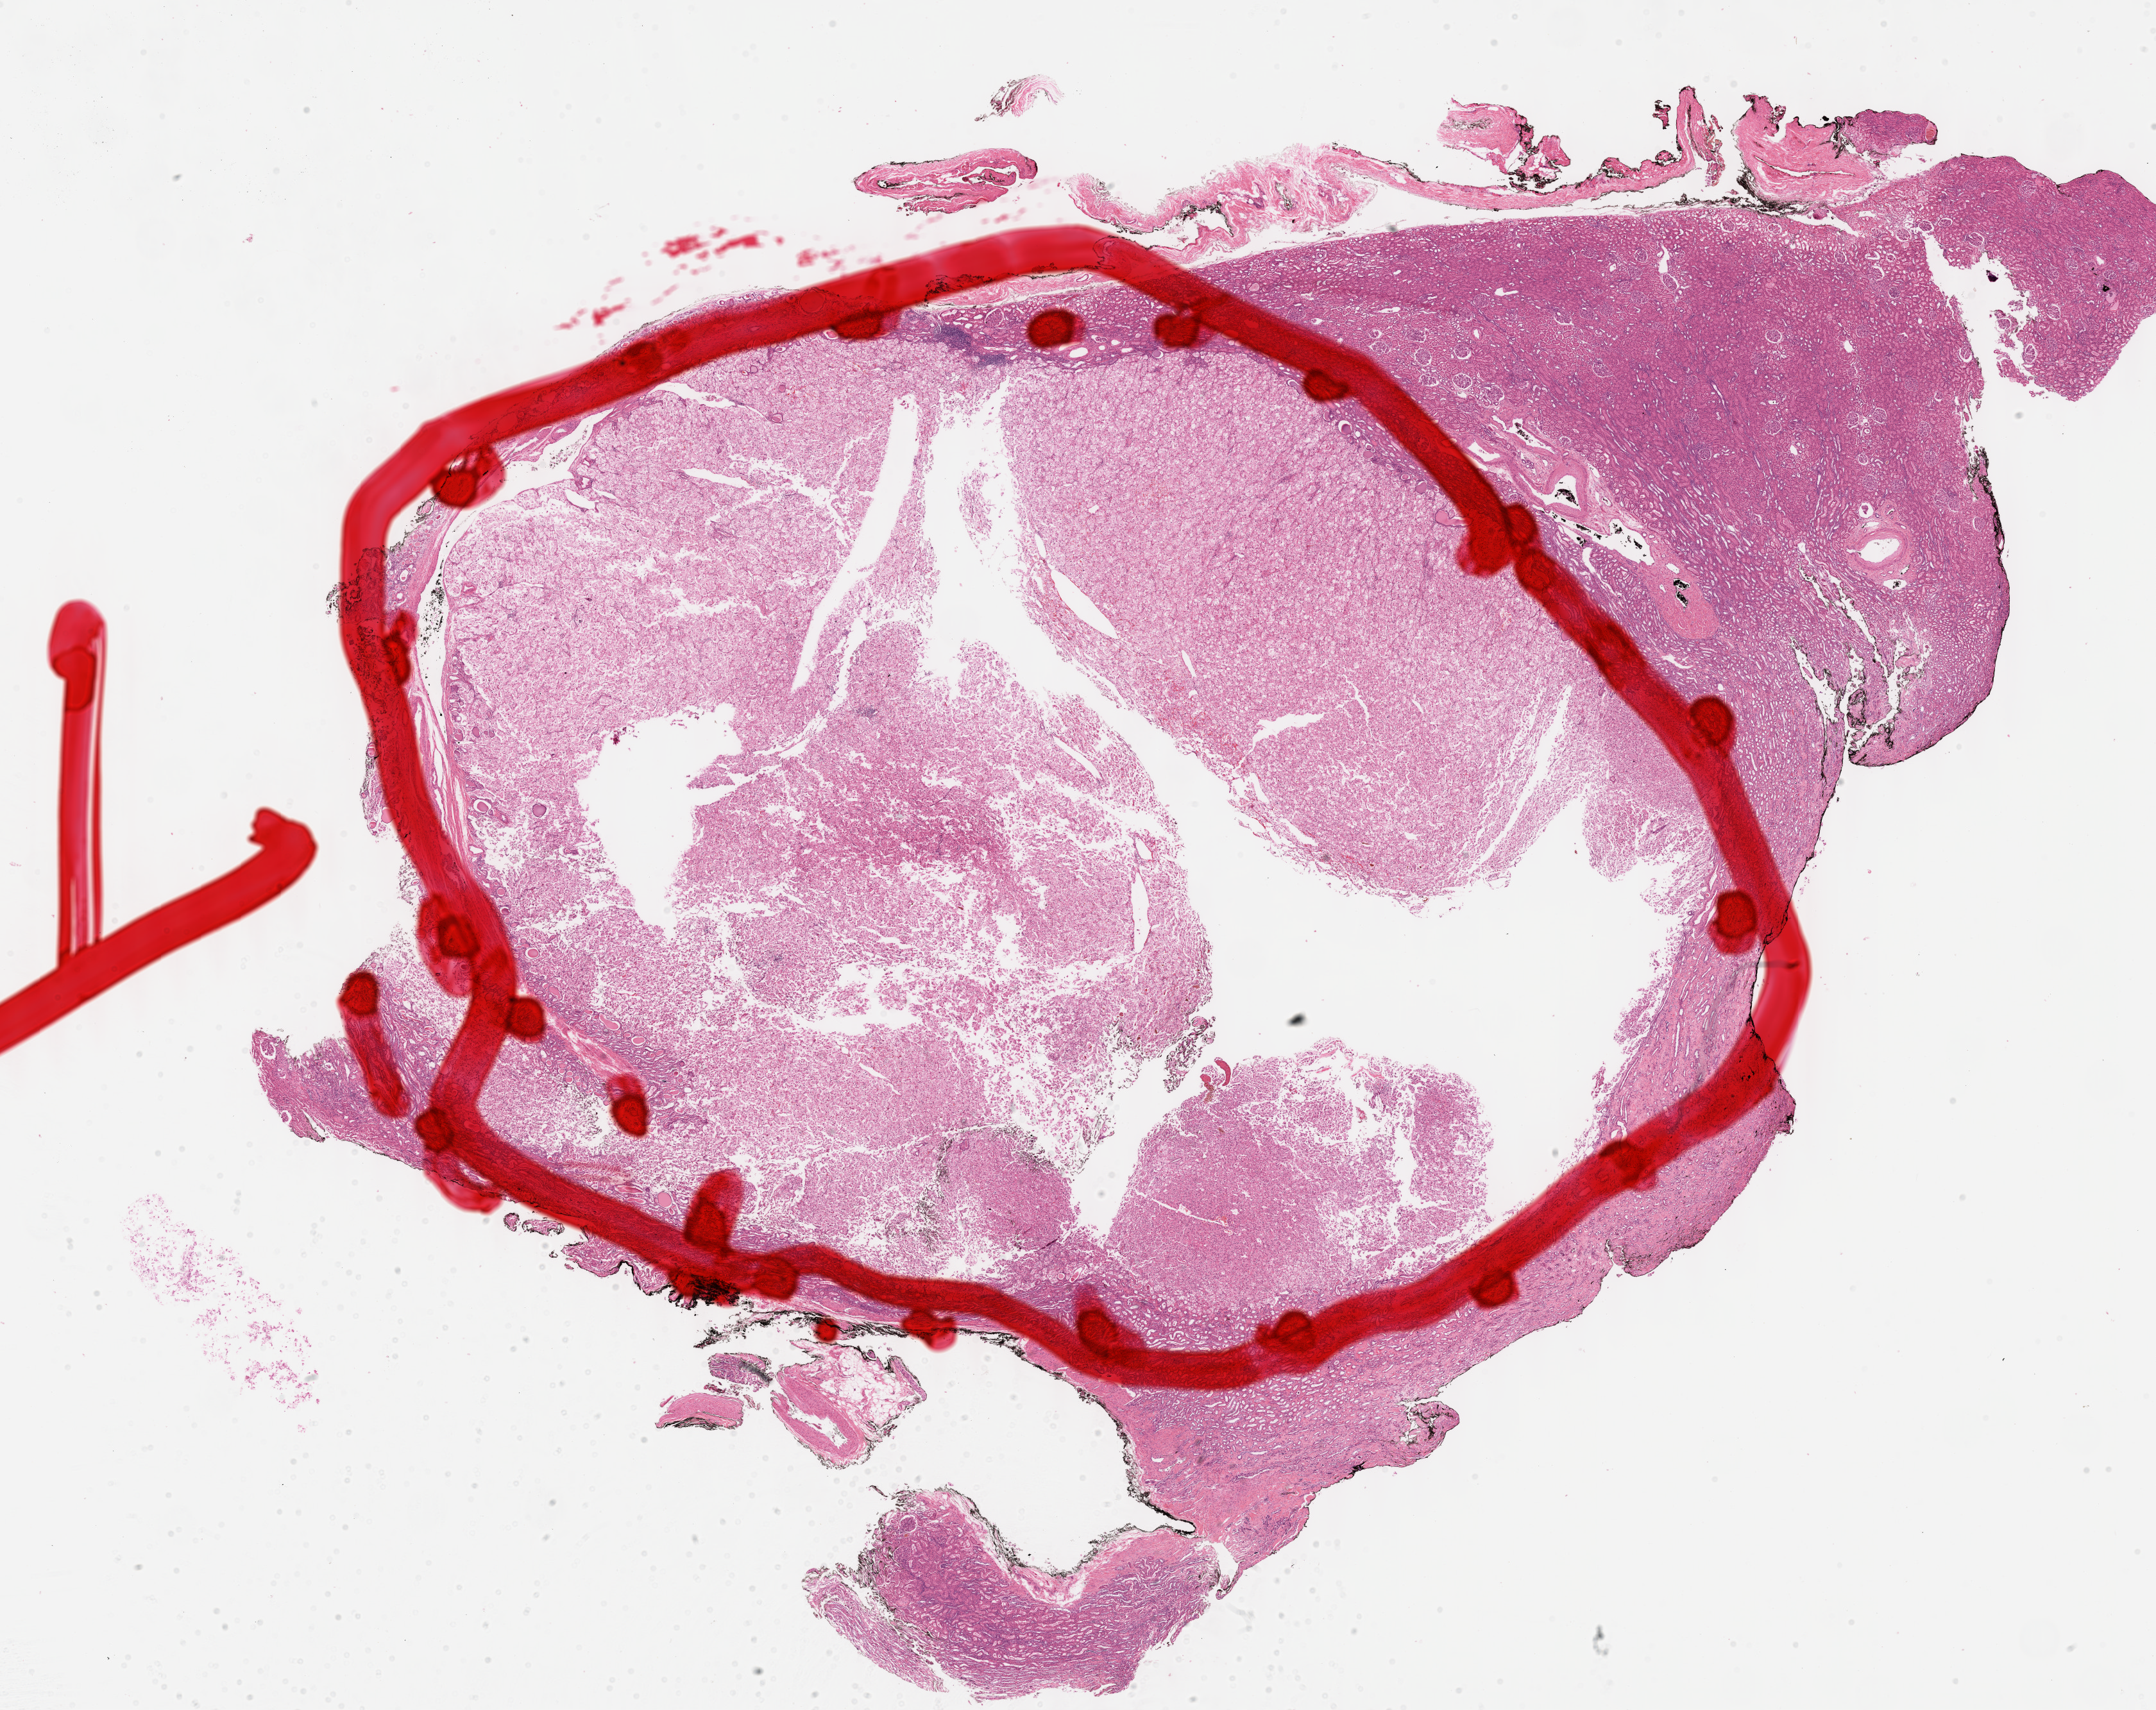
H&E-stained whole-slide image — low-resolution overview of the scanned area, about 27.2 x 21.5 mm (acquisition: 40x scan); FFPE section; primary tumour sample from the kidney. Patient: female, age at initial diagnosis 57 years. Pathologist review of this section (percent, as recorded): tumour cells 86%, tumour nuclei 86%, normal cells 9%, stromal cells 5%, necrosis 0%. Infiltration values recorded for this section: lymphocyte infiltration 5%, monocyte infiltration 1%, neutrophil infiltration 1%.
Laterality: left. AJCC pathologic stage: I (7th edition). Diagnosis: Renal cell carcinoma, chromophobe type.